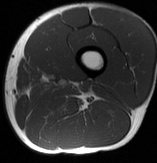
MRI of an extremity soft-tissue mass, one axial slice. Slice 14 of 70 in the series (ordered by position). MR volume resampled by the dataset authors to the PET/CT grid (not the native acquisition matrix). 3.27 mm slice thickness. 157 × 163 image matrix, field of view 153 × 159 mm. Male patient. From the clinical record (not read from this slice): histological type: extraskeletal osteosarcoma; grade: high; site of the primary tumour: left adductur.
Outlined on this slice (expert contour drawn on MRI and transferred to this co-registered scan by the dataset authors):
- gross tumour volume (mass): bounding box [x1, y1, x2, y2] px = [74, 81, 91, 93]